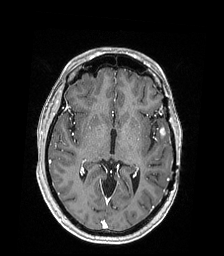
Brain MRI from a brain-tumour surgery series, one axial slice. Position 104 of 168 along the scan axis. T1-weighted post-contrast. 224 × 256 image matrix. From the clinical record (not read from this slice): histopathology: Astrocytoma; WHO grade: 4; IDH mutation: yes.
Annotated regions visible in this slice (manually delineated by an expert):
- tumour: bounding box [x1, y1, x2, y2] px = [160, 126, 165, 136]